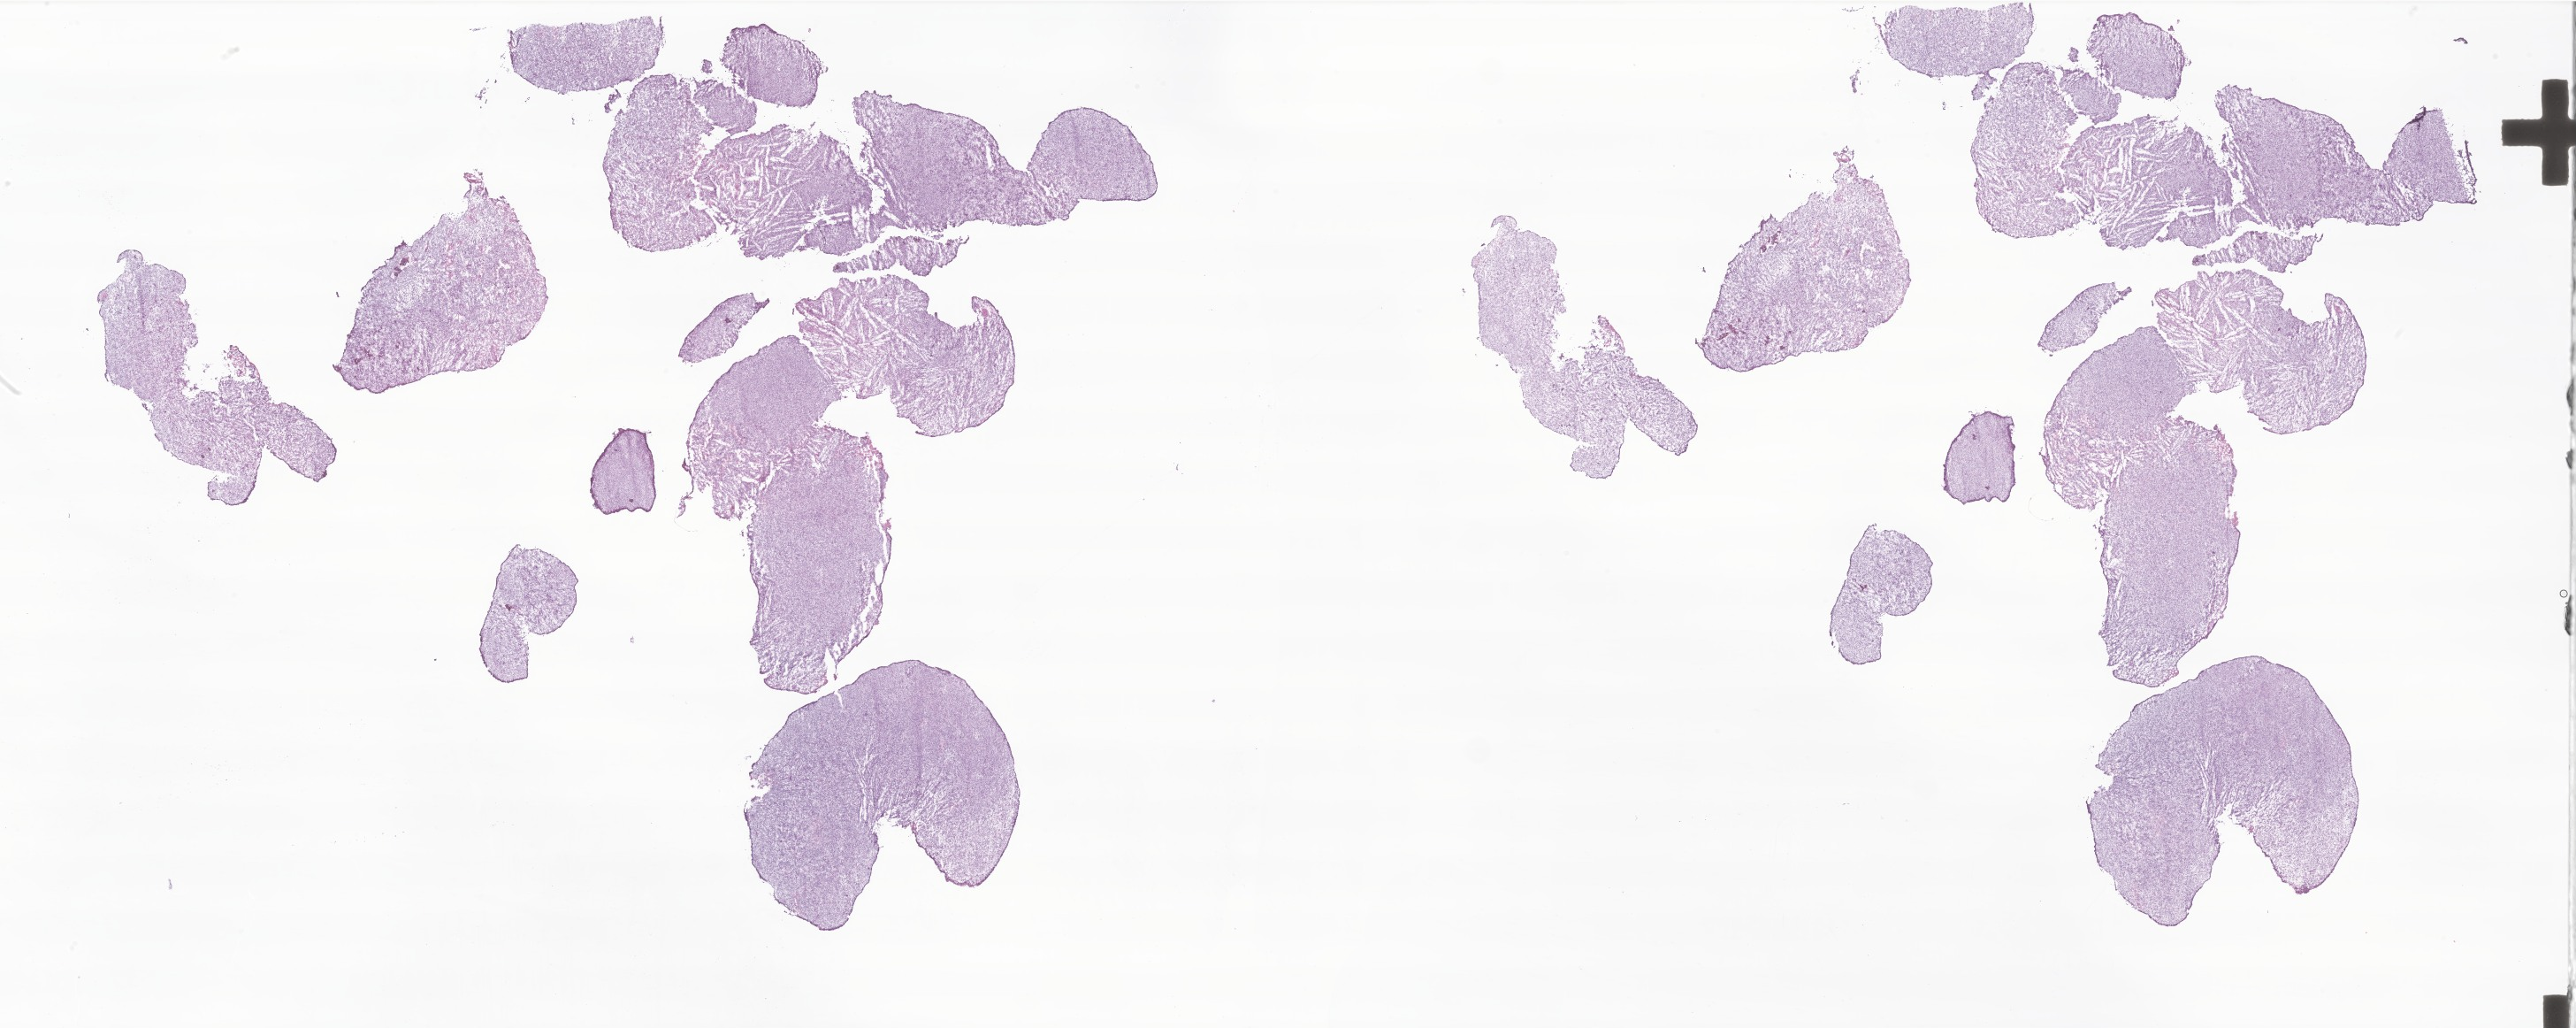
H&E whole-slide image of tumor tissue from the brain — low-resolution overview of the scanned area, about 49.1 x 19.6 mm. Frozen section. Patient male; age 201 months (16 years 9 months).
Diagnosis: Neoplasm, uncertain whether benign or malignant.